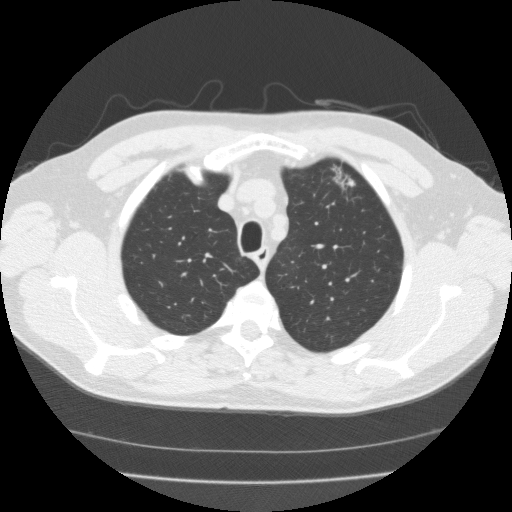
Low-dose screening chest CT, axial slice, third screening round (two years after baseline), lung window (W 1500 / L -600 HU), 2 mm slice thickness, standard (soft-tissue) reconstruction kernel (FC01), 120 kVp, slice 36 of 167 in the series, 512 × 512 image matrix. Male, age 56 years at enrolment. Former smoker at enrolment.
• Expert-annotated lung lesion, bounding box [x1, y1, x2, y2] px = [318, 158, 364, 199].
• Screening reader's record for this exam (one nodule recorded; not confirmed to be the boxed lesion): non-calcified nodule or mass ≥4 mm, left upper lobe, 18 × 10 mm, spiculated (stellate) margins, soft tissue attenuation, pre-existing on the prior screen: yes; interval growth: yes.
• Official screen result: positive, other.
• Participant outcome: lung cancer diagnosed 119 days after this screen — adenocarcinoma, NOS, left upper lobe, moderately differentiated (G2), stage IA (AJCC 6th edition), 15 mm at pathology.